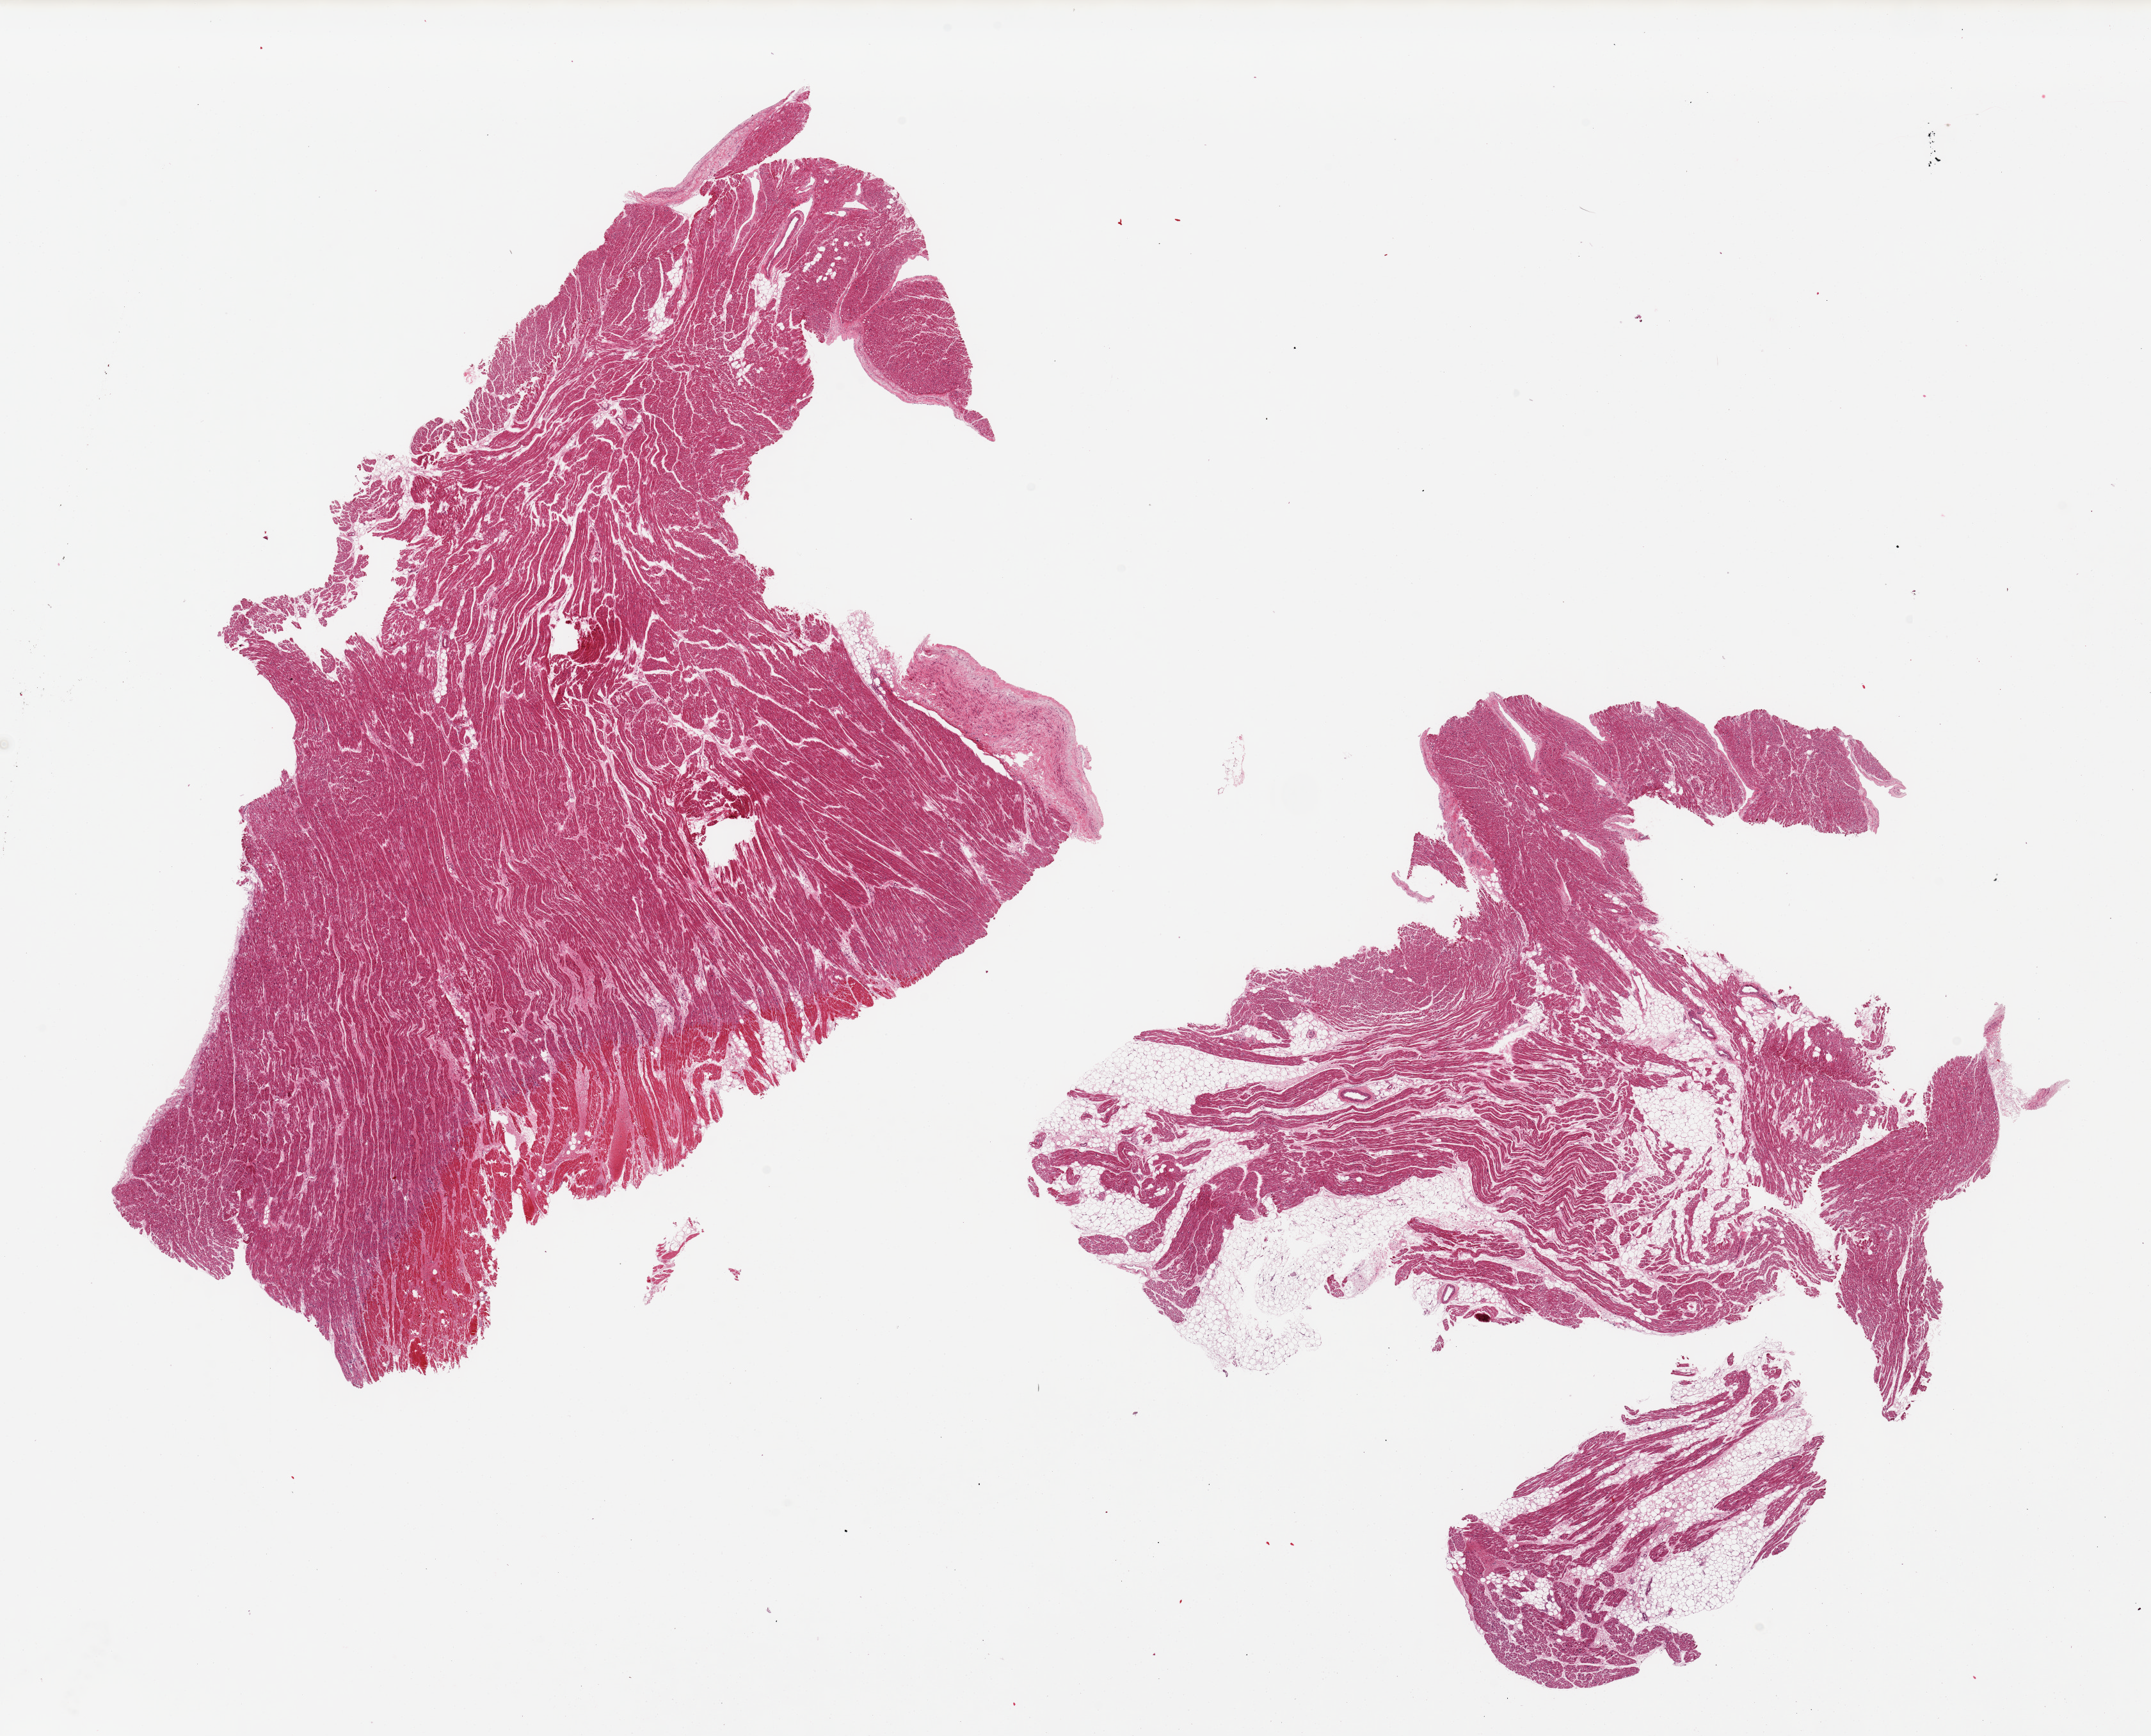
Whole-slide image, hematoxylin and eosin (H&E) stain, brightfield — shown as a low-resolution overview of the whole scanned area (about 26.6 x 21.5 mm). PAXgene-fixed, paraffin-embedded tissue. Section of auricular appendage (target tissue). Tissue donor sample. Male donor.
Pathologist's review note for this sample: 2 pieces, one ~30% adipose tissue; contraction bands and hemorrhage, polys and early coagulation necrosis suggestive of acute infarction.